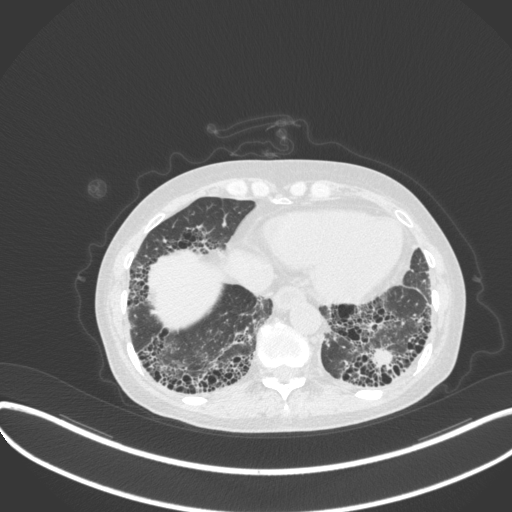
Chest CT, one axial slice. Slice 70 of 373 in the series (ordered by position). Reconstruction kernel B31f. 120 kVp. Lung window (W 1500 / L -600 HU). 512 × 512 image matrix, field of view 400 × 400 mm. Female patient, age 56 years. Case-level facts recorded for this patient, not image findings: clinical TNM (as recorded): T1 N0 M0.
Annotated regions visible in this slice (bounding box drawn by a radiologist):
- lung tumour (recorded histology: adenocarcinoma): bounding box (x1, y1, x2, y2) in pixels: (363, 347, 398, 372)